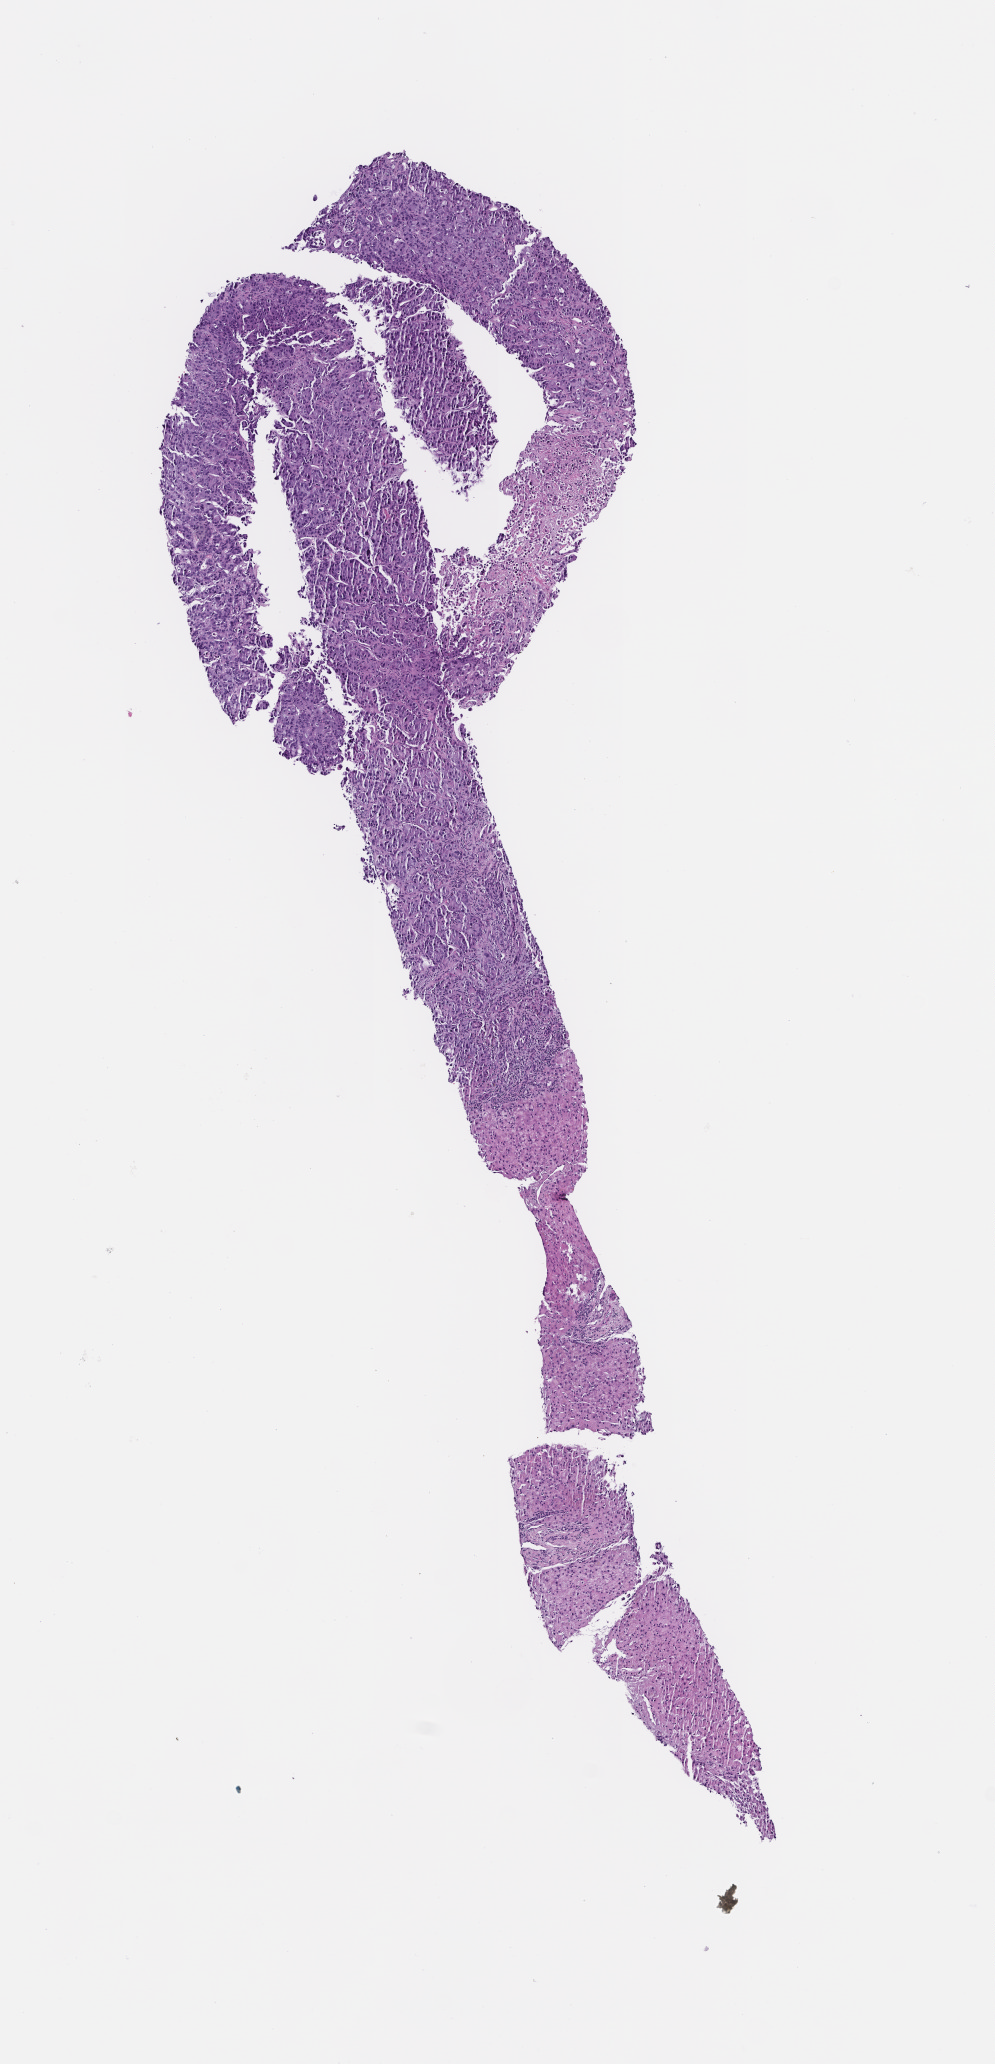
Haematoxylin and eosin whole-slide image — shown as a low-resolution overview of the whole scanned area (about 4.0 x 8.3 mm), FFPE section, archival tissue. Female patient.
This section: metastasis (sampled organ not recorded). Primary diagnosis of the patient: Non-Small Cell Lung Carcinoma.